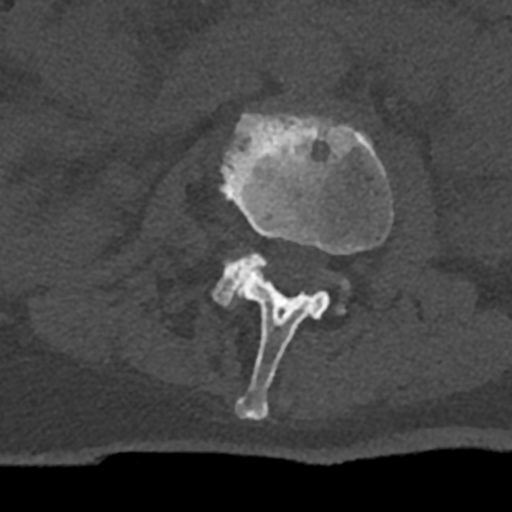
CT including the spine, one axial slice. Slice 361 of 797 in the series (ordered by position). Reconstruction kernel Br40s/3. Bone window (W 1800 / L 400 HU). 0.5 mm slice thickness. 512 × 512 image matrix, field of view 160 × 160 mm. Male patient, age 74 years. Case-level facts recorded for this patient, not image findings: primary cancer: renal; vertebrae with lytic lesions (as recorded): T10, L1, L2, L3, L4, L5.
Structures marked on this image (semi-automatic segmentation, software-assisted and operator-edited):
- L2 vertebra: bounding box <220,113,393,421> (left, top, right, bottom; pixels)
- L3 vertebra: <213,253,349,313>